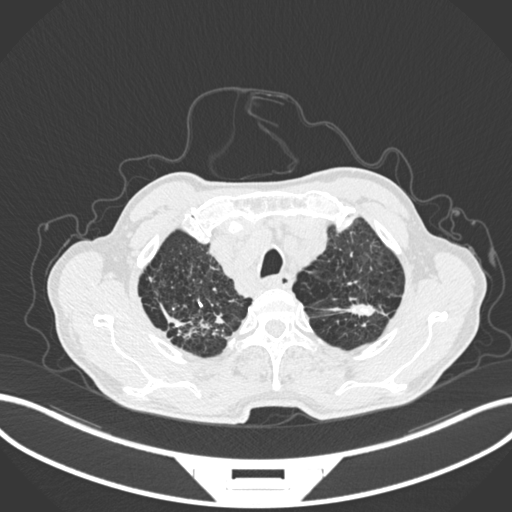
Chest CT, one axial slice; position 239 of 287 along the scan axis; reconstruction kernel B30f; 120 kVp; lung window (W 1500 / L -600 HU); 1 mm slice thickness; 512 × 512 image matrix. Patient: male, 74 years. From the clinical record (not read from this slice): clinical TNM (as recorded): T2a N1 M0.
Annotated regions visible in this slice (bounding box drawn by a radiologist):
- lung tumour (recorded histology: adenocarcinoma): bounding box (x1, y1, x2, y2) in pixels: (333, 299, 376, 319)